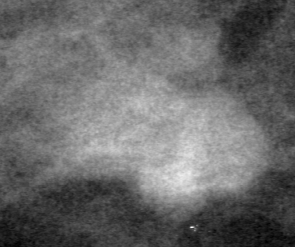
Cropped region of a digitized screen-film mammogram centred on a radiologist-marked abnormality; right breast; MLO view.
Marked abnormality: mass, shape lobulated, margins obscured; BI-RADS assessment category 3; pathology result (as recorded, not read from the image): benign.